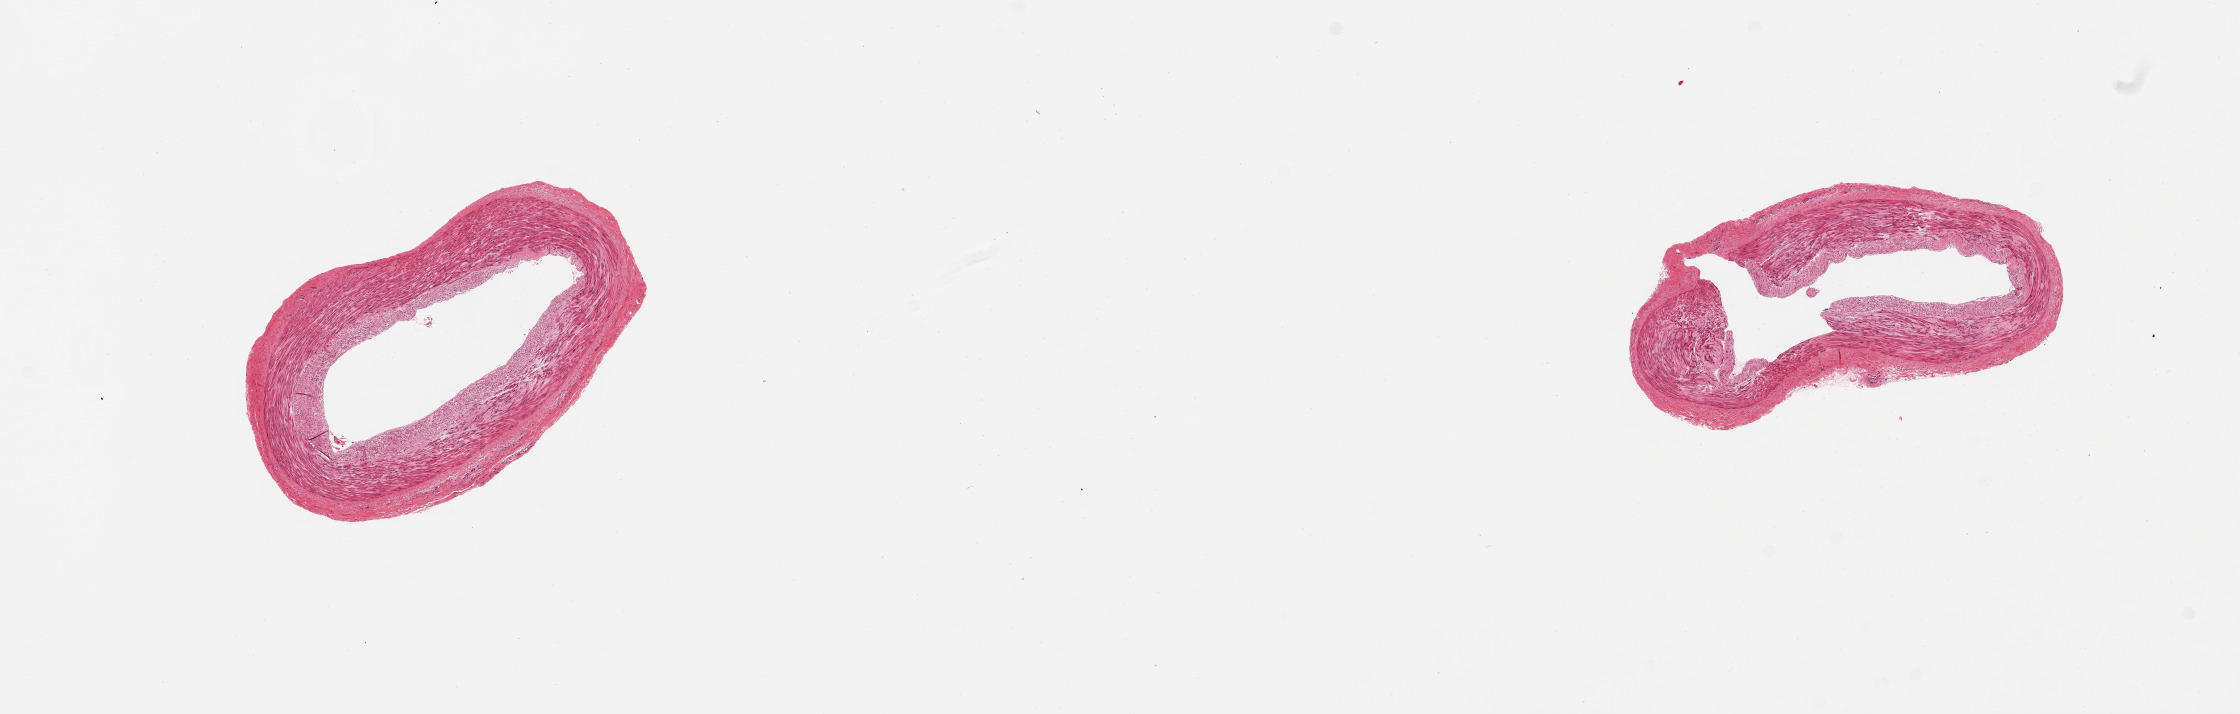
Digitized H&E-stained section, brightfield, whole scanned area (about 17.7 x 5.6 mm) shown as a low-resolution overview, PAXgene-fixed, paraffin-embedded tissue, section of tibial artery (target tissue), donor tissue sample. Male donor.
- pathologist's review note for this sample: 2 pieces; well trimmed; no lesions